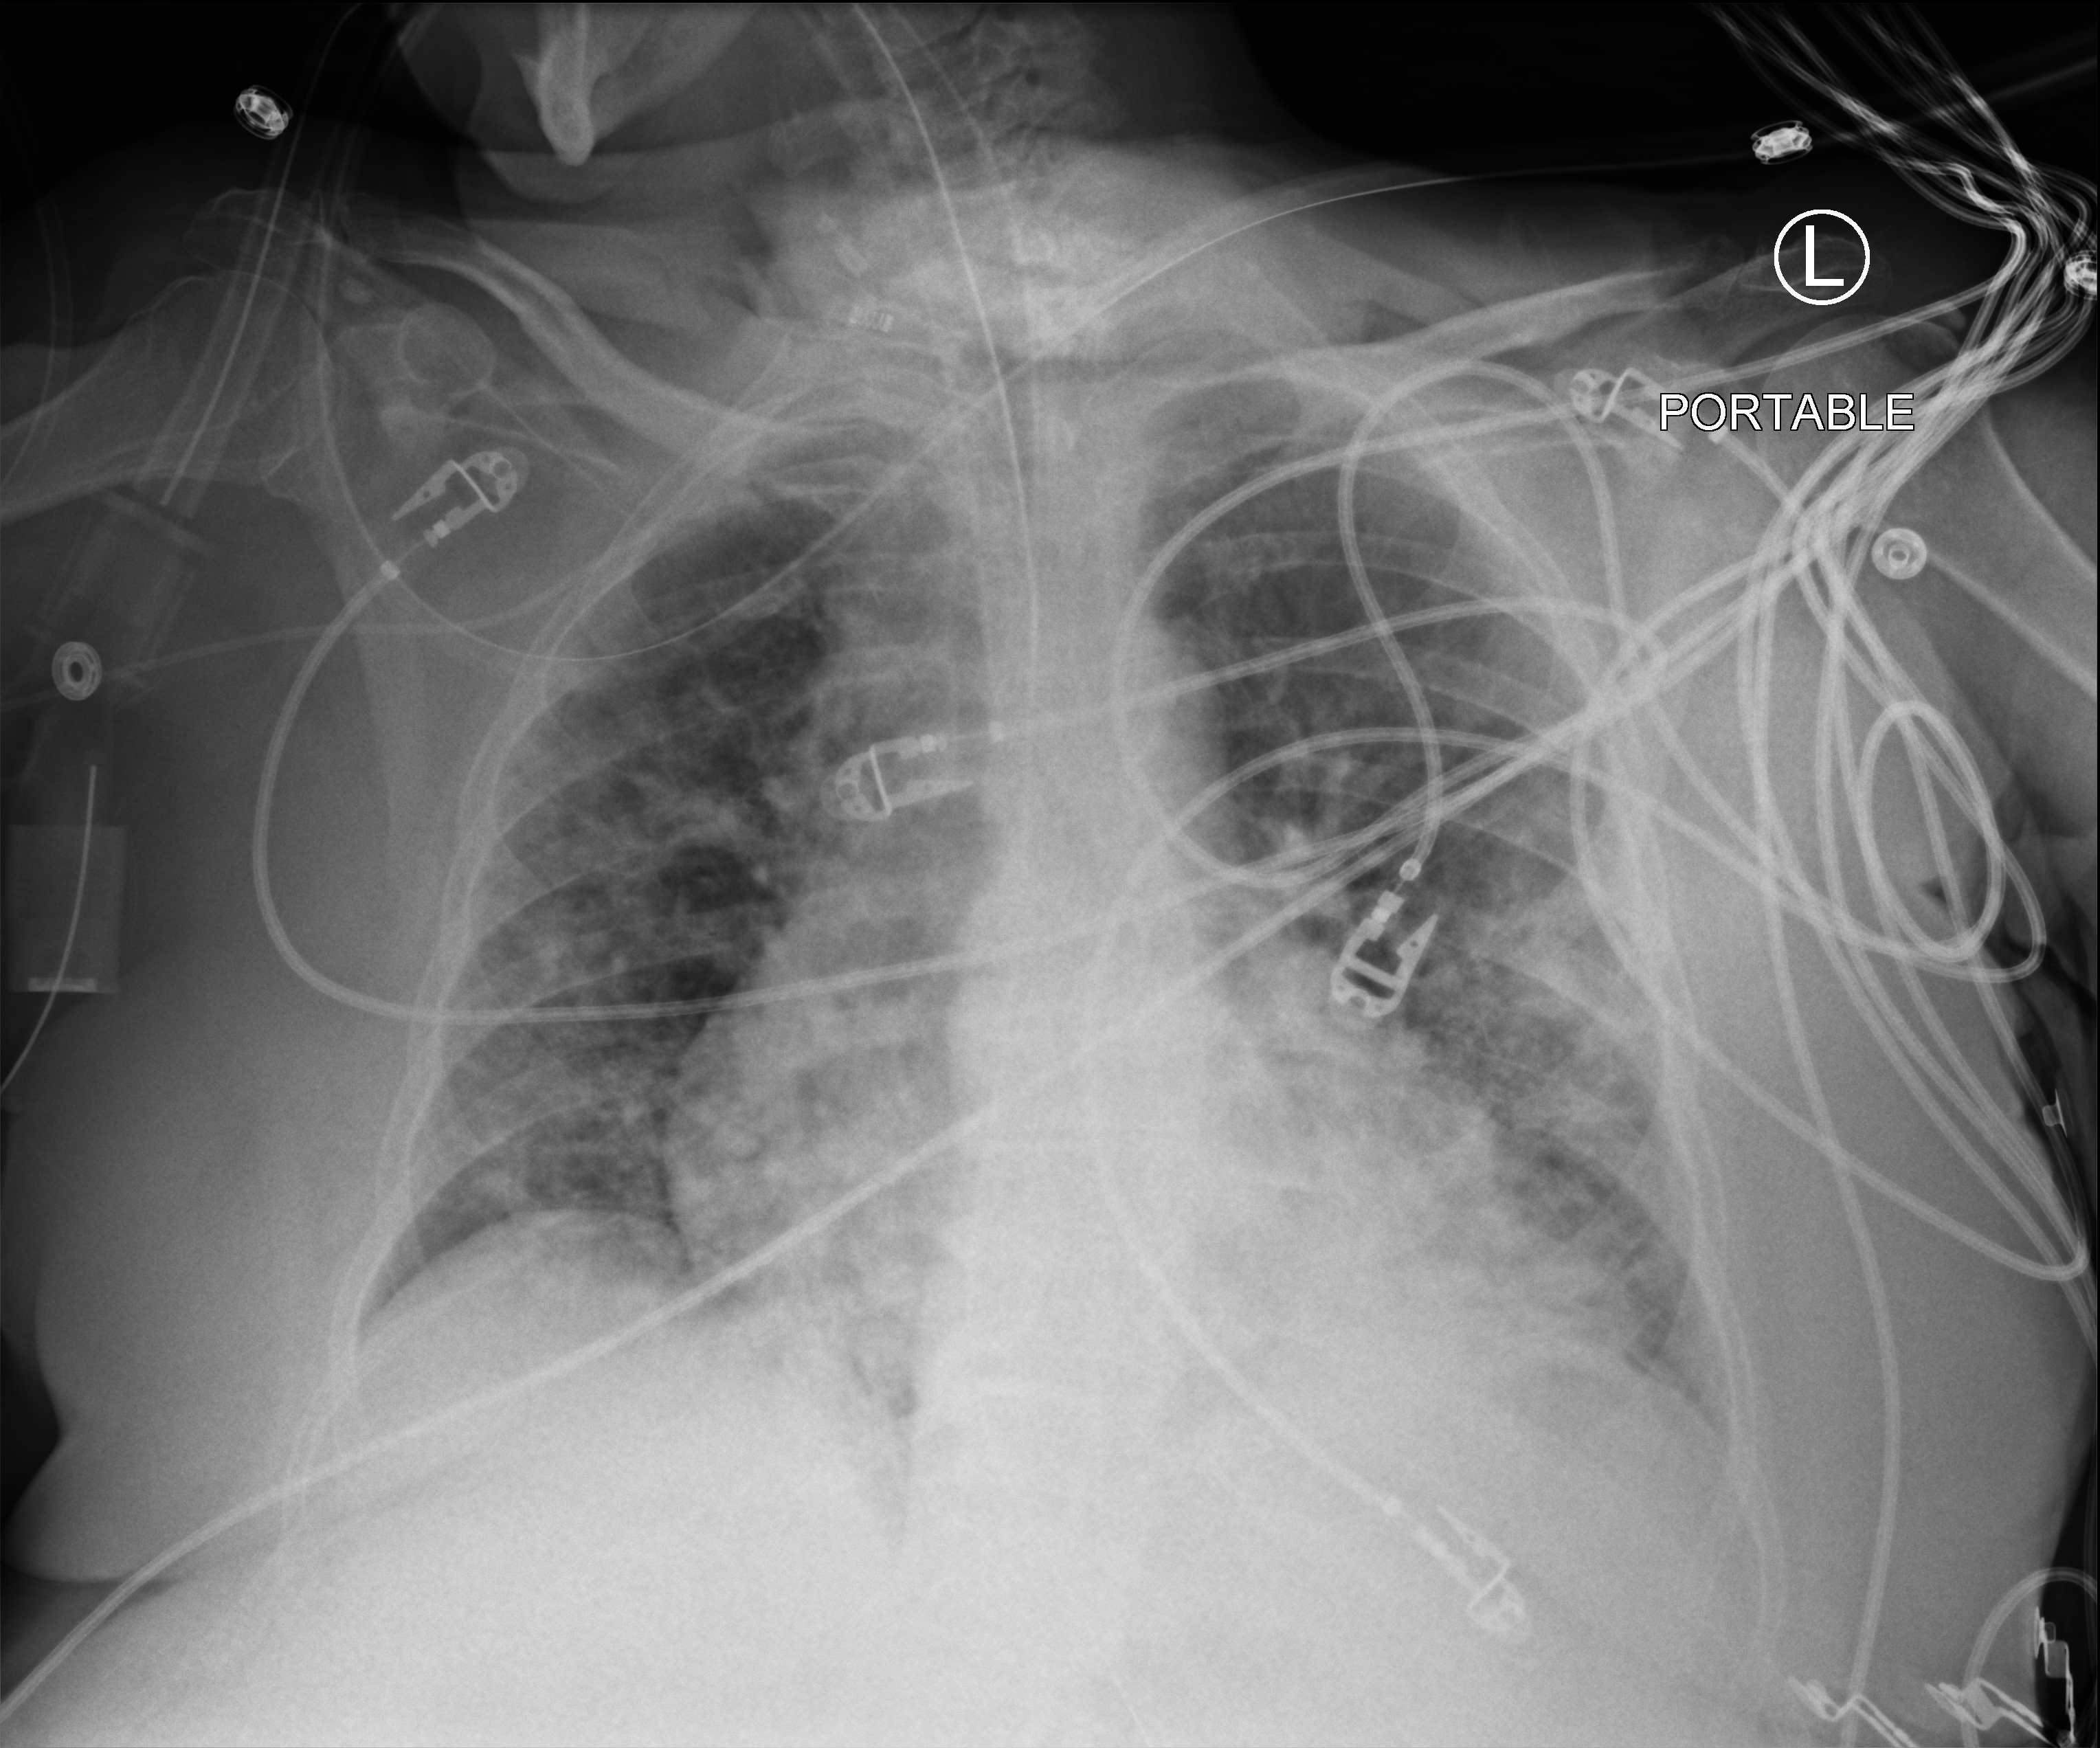
Chest X-ray (portable), anteroposterior (AP) projection. Female patient hospitalised with COVID-19, age 75–90 years.
From the hospital-stay record, not from the radiograph (when in the stay this image was taken is not recorded): length of hospital stay: 31 days; diabetes (admission record): no.